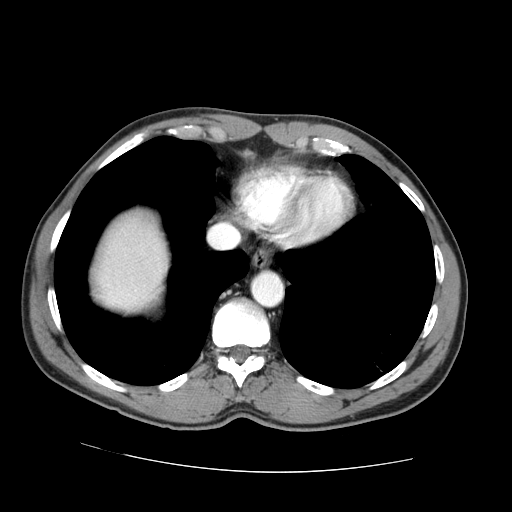
Contrast-enhanced abdominal CT (liver protocol), one axial slice. Position 65 of 73 along the scan axis. Reconstruction kernel STANDARD. One of 2 acquisitions stored at this slice position. Soft-tissue window (W 400 / L 40 HU). 2.5 mm slice thickness. 512 × 512 image matrix, field of view 380 × 380 mm. Case-level facts recorded for this patient, not image findings: diagnosis: hepatocellular carcinoma (patient treated with transarterial chemoembolisation; whether this scan precedes or follows treatment is not stated here); TNM stage (as recorded): Stage-IVA; Child-Pugh class: A; tumour differentiation: no biopsy.
Structures marked on this image (semi-automatic segmentation, software-assisted and operator-edited):
- abdominal aorta: box from (x=253, y=272) to (x=282, y=305) px
- liver parenchyma outside the tumour (the mass and vessels are separate outlines, so this box may not span the whole liver): (x=92, y=216)–(x=168, y=310)